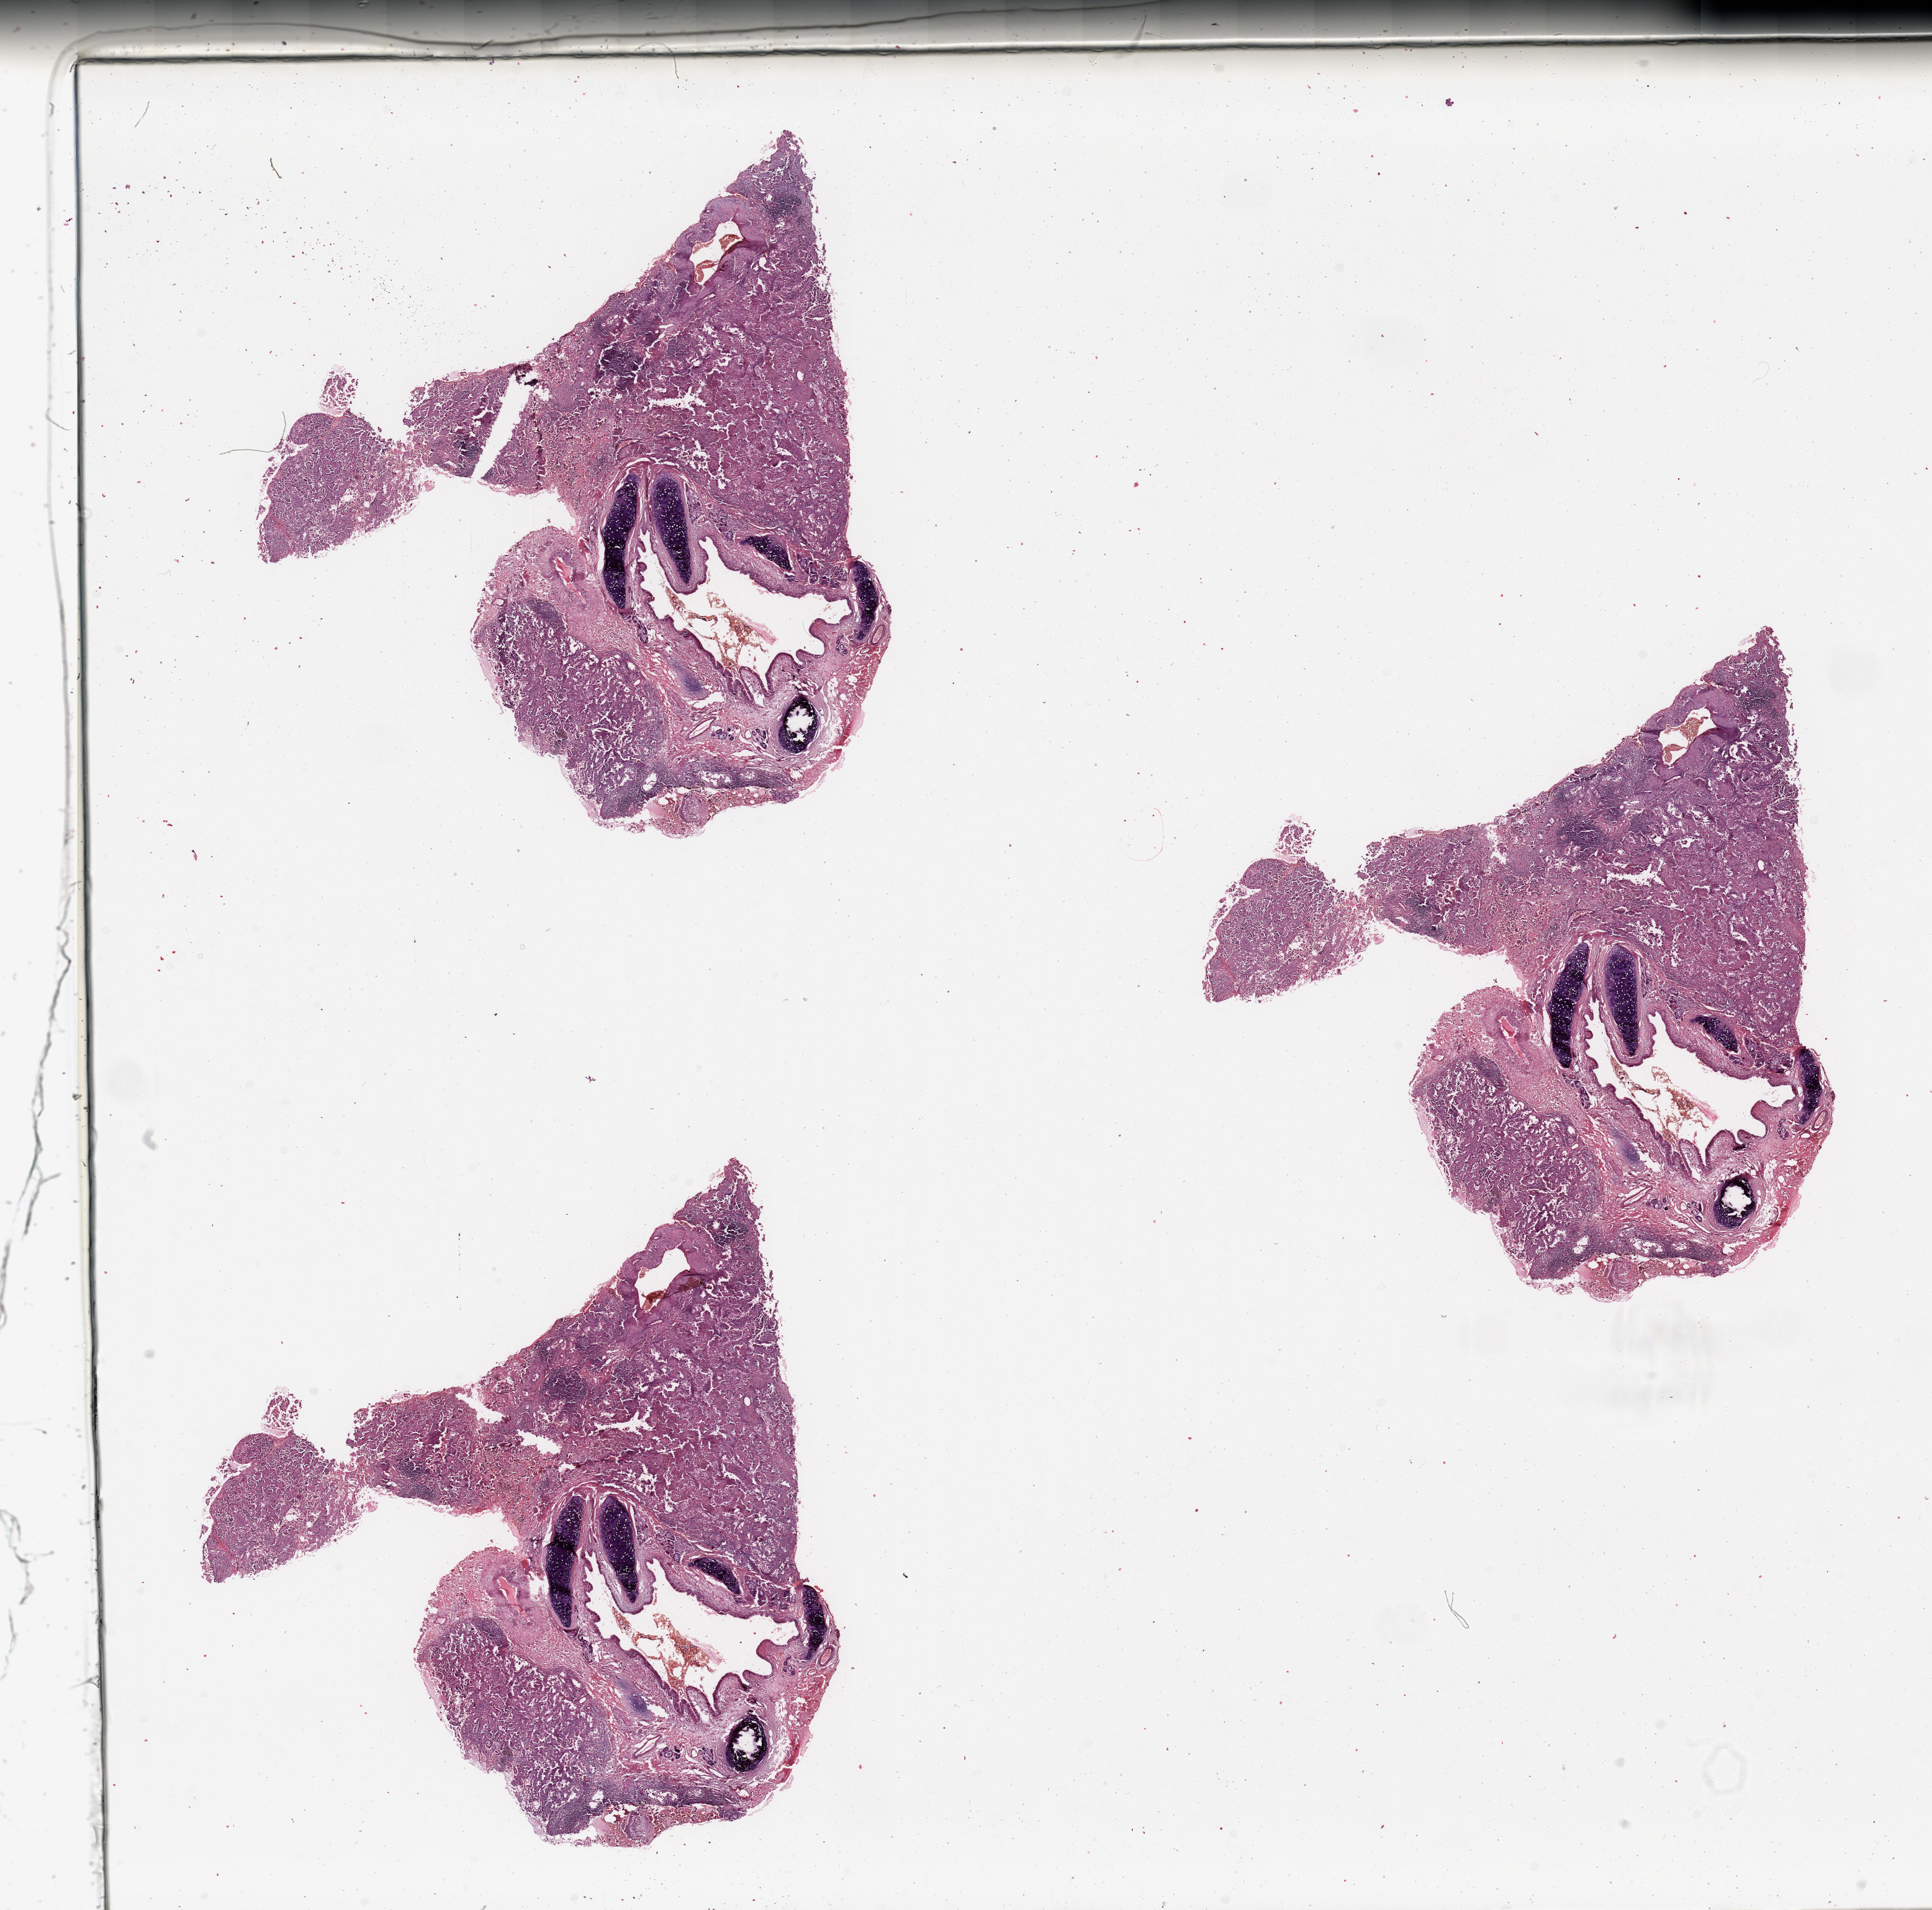
Digitized Hematoxylin and eosin (H&E) stained tissue section (whole slide), shown as a low-resolution overview of the whole scanned area (about 24.6 x 24.3 mm); lung, tumour tissue. 73-year-old female patient. Histologic grade: G2 (moderately differentiated).
• diagnosis: Adenocarcinoma, NOS
• primary tumour site (as recorded): right upper lobe
• AJCC pathologic stage: IB